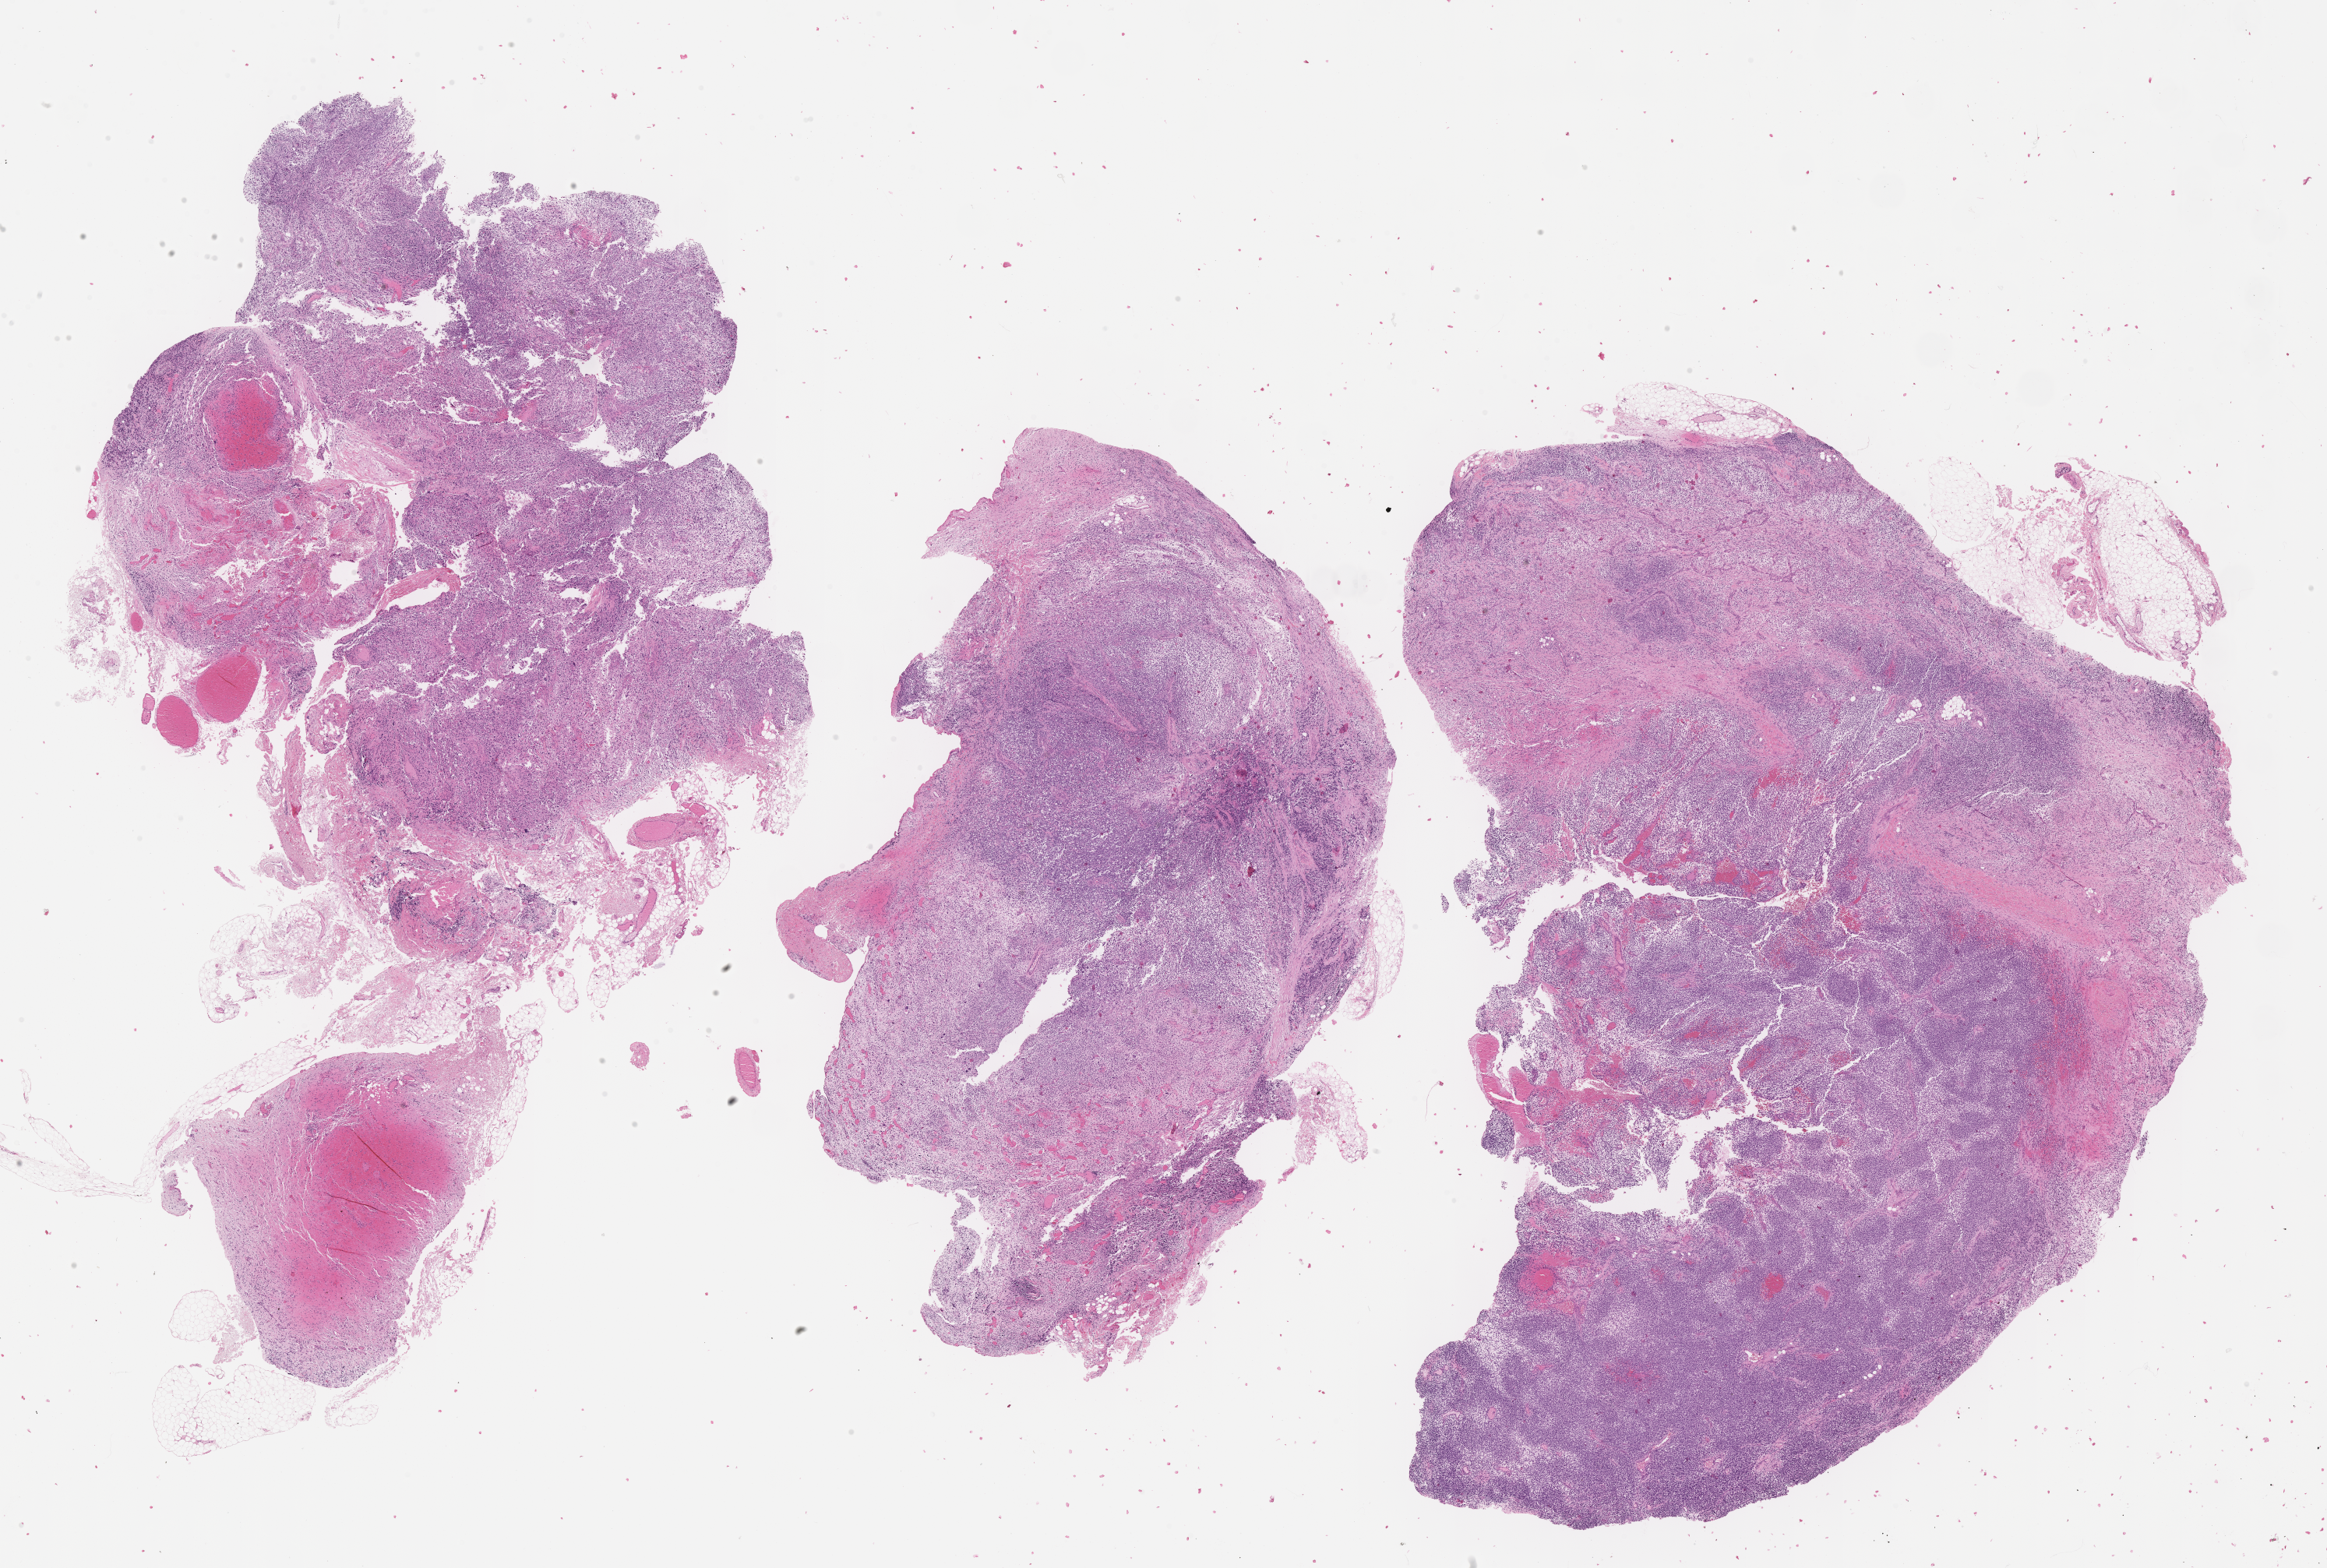
Hematoxylin and eosin (H&E) whole-slide image of tumor tissue, whole scanned area (about 24.2 x 16.3 mm) shown as a low-resolution overview; formalin-fixed, paraffin-embedded (FFPE) tissue; sample anatomic site: eye, orbit-left medial. Patient: male, age 13.9 years at diagnosis.
• metastatic status at presentation (as recorded): non-metastatic
• diagnosis: rhabdomyosarcoma; histological classification: embryonal rhabdomyosarcoma
• stage (as recorded): 1